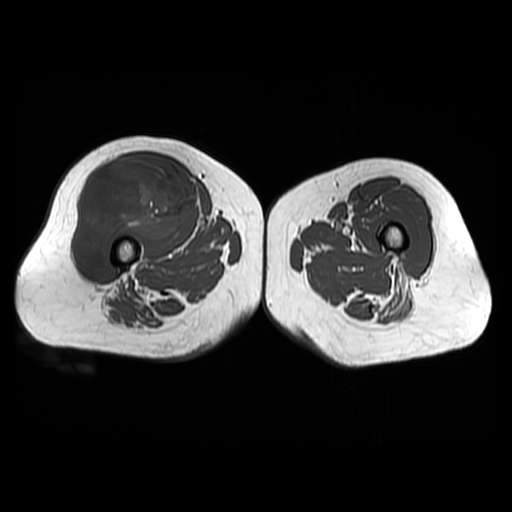
MRI of an extremity soft-tissue mass, one axial slice. Position 30 of 48 along the scan axis. 6 mm slice thickness. 512 × 512 image matrix, field of view 440 × 440 mm. Female patient. From the clinical record (not read from this slice): histological type: pleiomorphic undifferentiated sarcoma; grade: high; site of the primary tumour: right quadricep.
Outlined on this slice (expert manual segmentation):
- gross tumour volume including surrounding oedema: bounding box [x1, y1, x2, y2] px = [73, 156, 195, 272]
- gross tumour volume (mass): [73, 156, 195, 272]